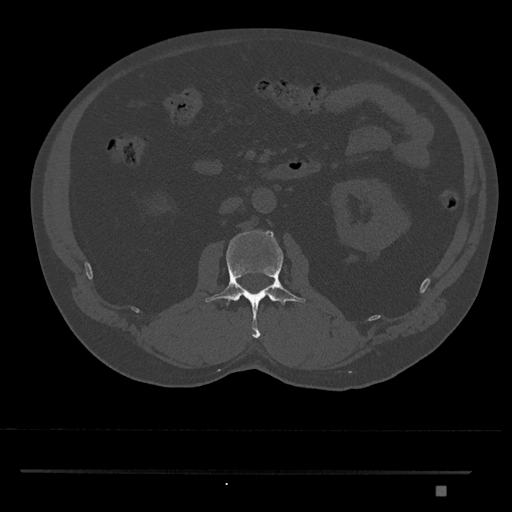
CT including the spine, one axial slice; position 752 of 1134 along the scan axis; reconstruction kernel Br40s/3; bone window (W 1800 / L 400 HU); 512 × 512 image matrix. Patient: male, 65 years. From the clinical record (not read from this slice): primary cancer: prostate.
Structures marked on this image (semi-automatically segmented with operator editing):
- L2 vertebra: bounding box <205,230,306,338> (left, top, right, bottom; pixels)